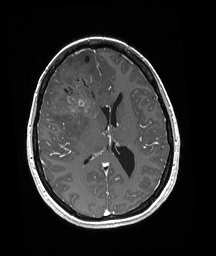
Brain MRI from a brain-tumour surgery series, one axial slice; position 88 of 192 along the scan axis; T1-weighted post-contrast; 1 mm slice thickness; 216 × 256 image matrix, field of view 211 × 250 mm. From the clinical record (not read from this slice): histopathology: Oligodendroglioma; WHO grade: 3; IDH mutation: yes.
Outlined on this slice (manually delineated by an expert):
- tumour: bounding box (x1, y1, x2, y2) in pixels: (52, 65, 102, 117)